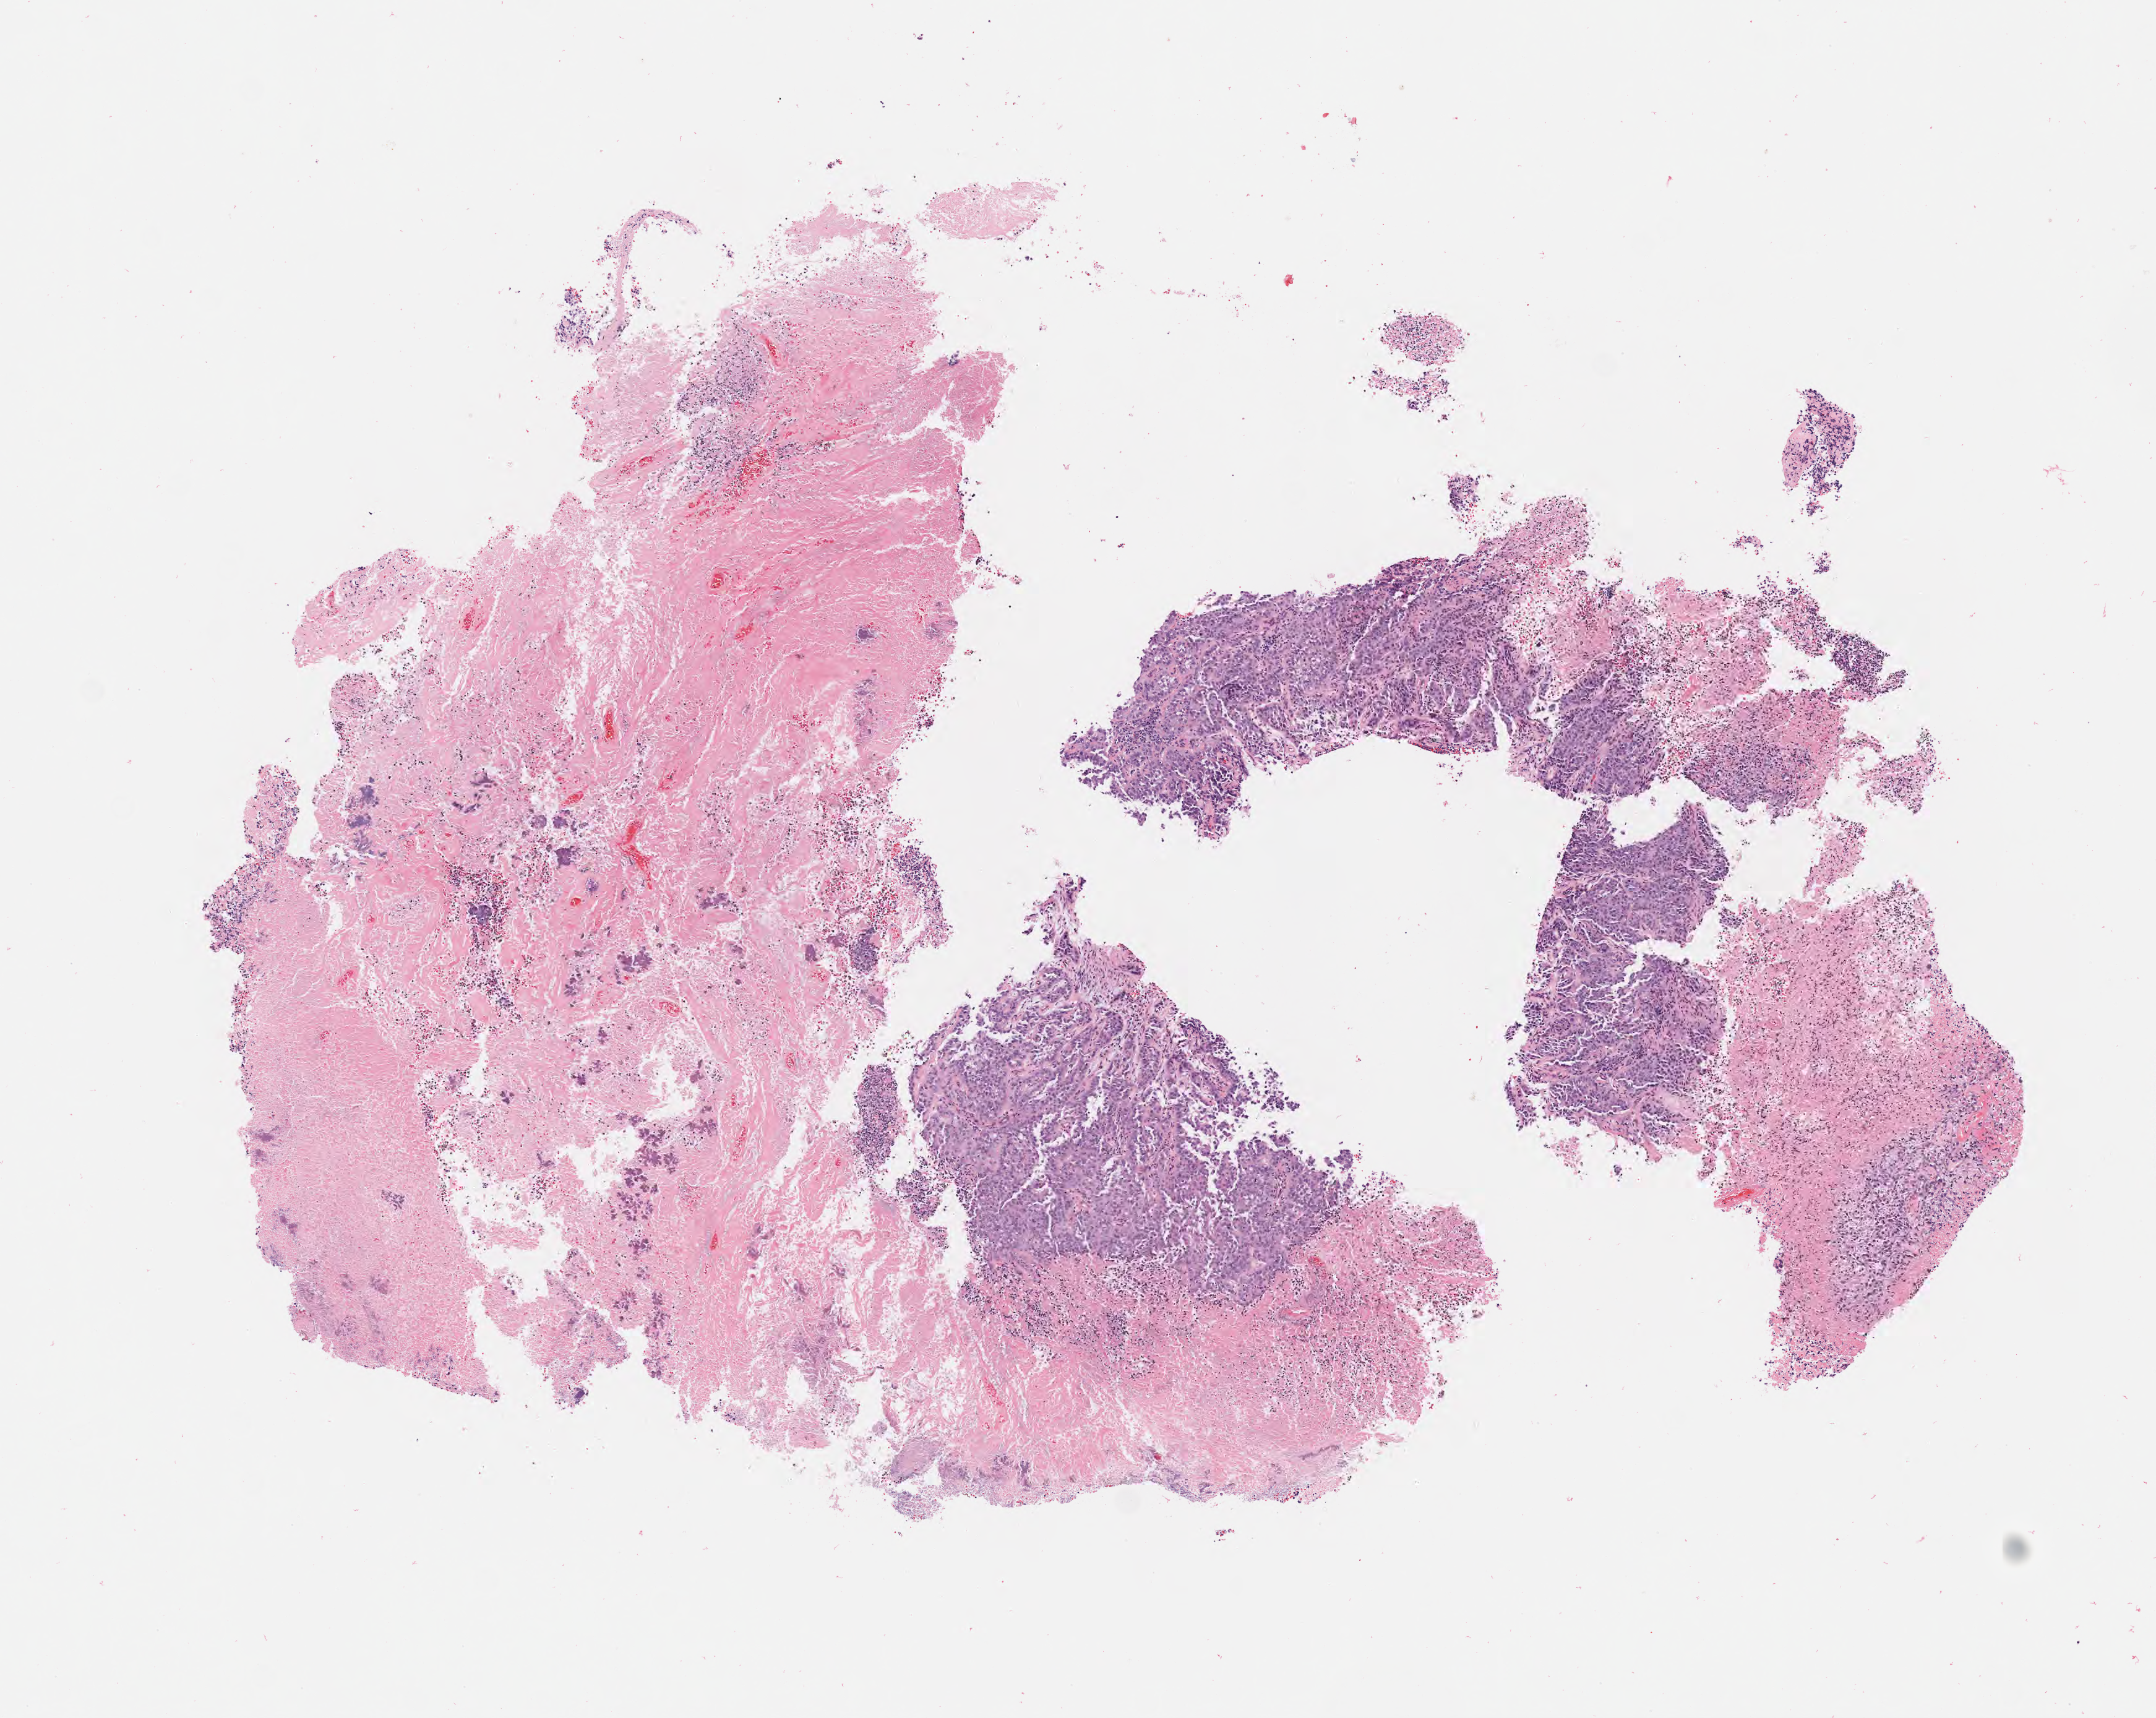
Digitized H&E-stained section — low-resolution overview of the scanned area, about 7.0 x 5.6 mm. Specimen: tumor tissue. Anatomic site: cervix. Female patient, age 51 years.
• diagnosis: Adenocarcinoma, NOS